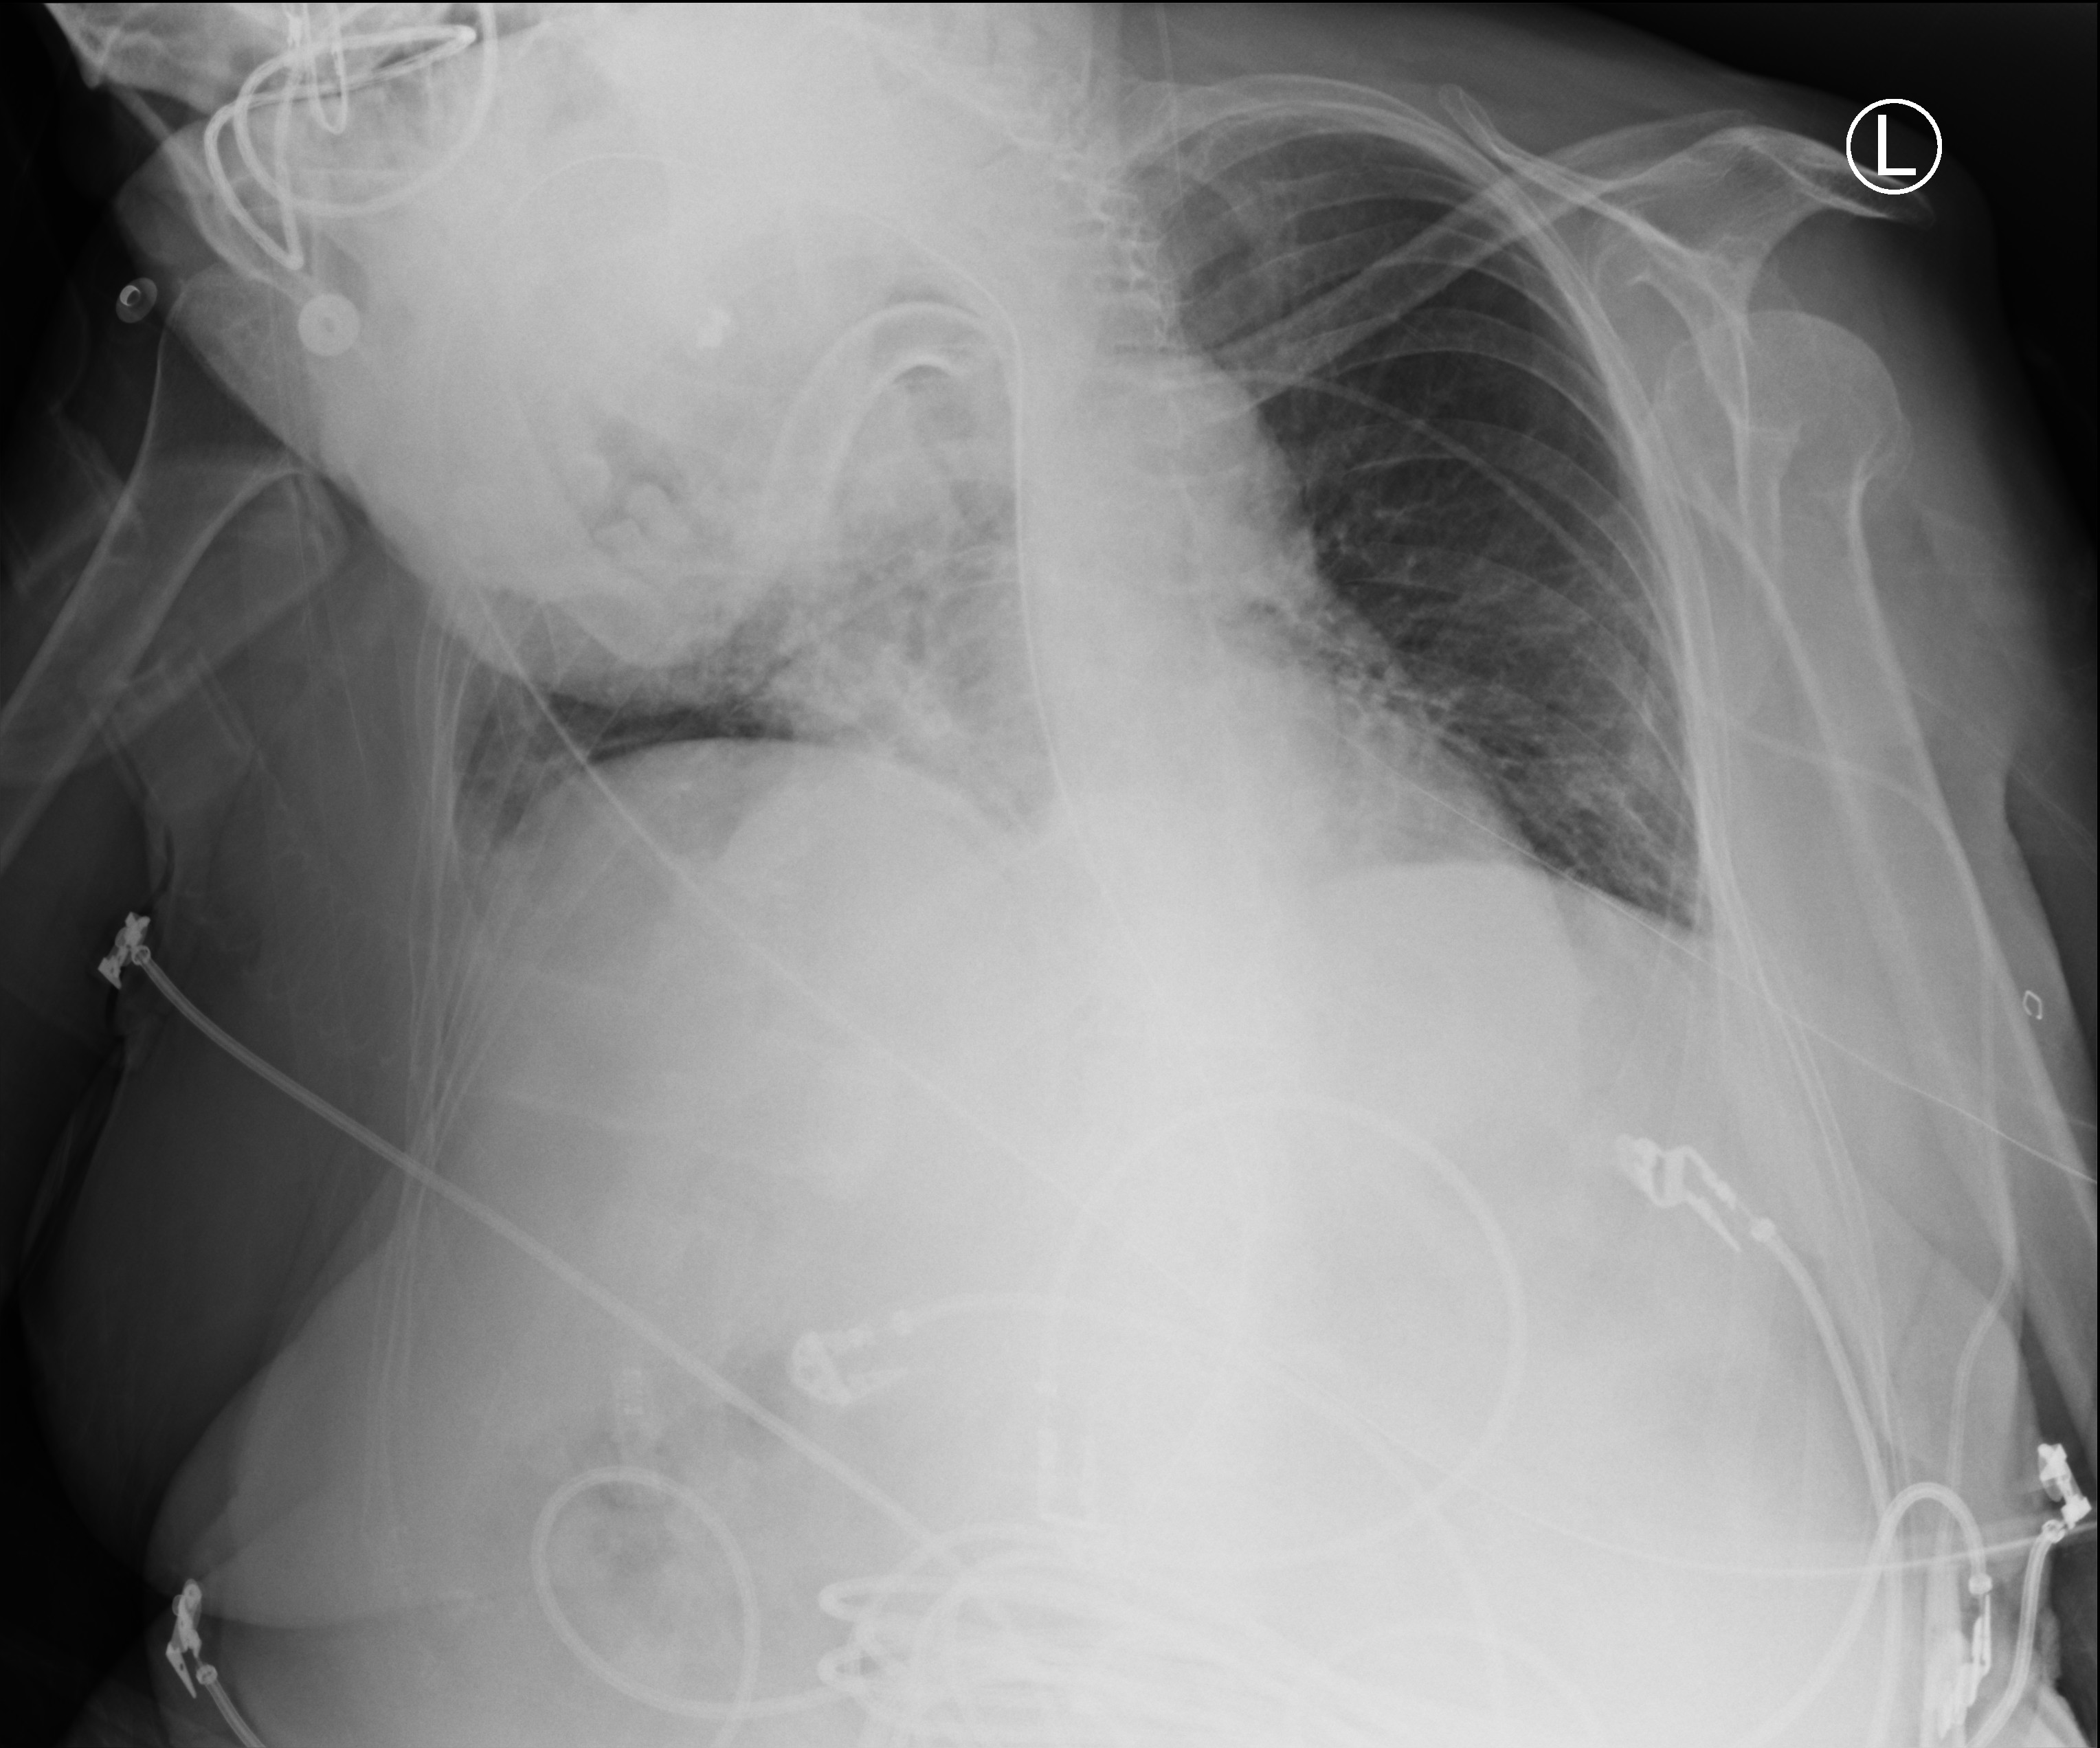
Bedside chest radiograph (computed radiography); anteroposterior (AP) projection. Patient hospitalised with COVID-19; female, aged 75–90 years.
From the hospital-stay record, not from the radiograph (when in the stay this image was taken is not recorded): smoking status (admission record): former; other chronic lung disease (admission record): yes.